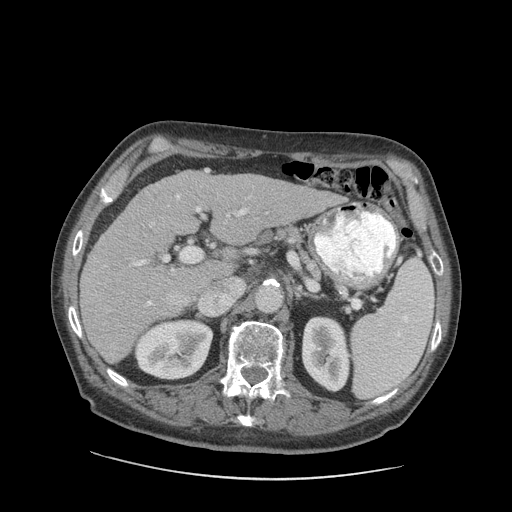
Contrast-enhanced abdominal CT (liver protocol), one axial slice; slice 51 of 89 in the series (ordered by position); reconstruction kernel STANDARD; 140 kVp; soft-tissue window (W 400 / L 40 HU); 2.5 mm slice thickness; 512 × 512 image matrix. From the clinical record (not read from this slice): diagnosis: hepatocellular carcinoma (patient treated with transarterial chemoembolisation; whether this scan precedes or follows treatment is not stated here); TNM stage (as recorded): Stage-I; Child-Pugh class: A.
Outlined on this slice (semi-automatic segmentation, software-assisted and operator-edited):
- liver parenchyma outside the tumour (the mass and vessels are separate outlines, so this box may not span the whole liver): bounding box (x1, y1, x2, y2) in pixels: (80, 170, 336, 364)
- liver vessels: (86, 171, 254, 307)